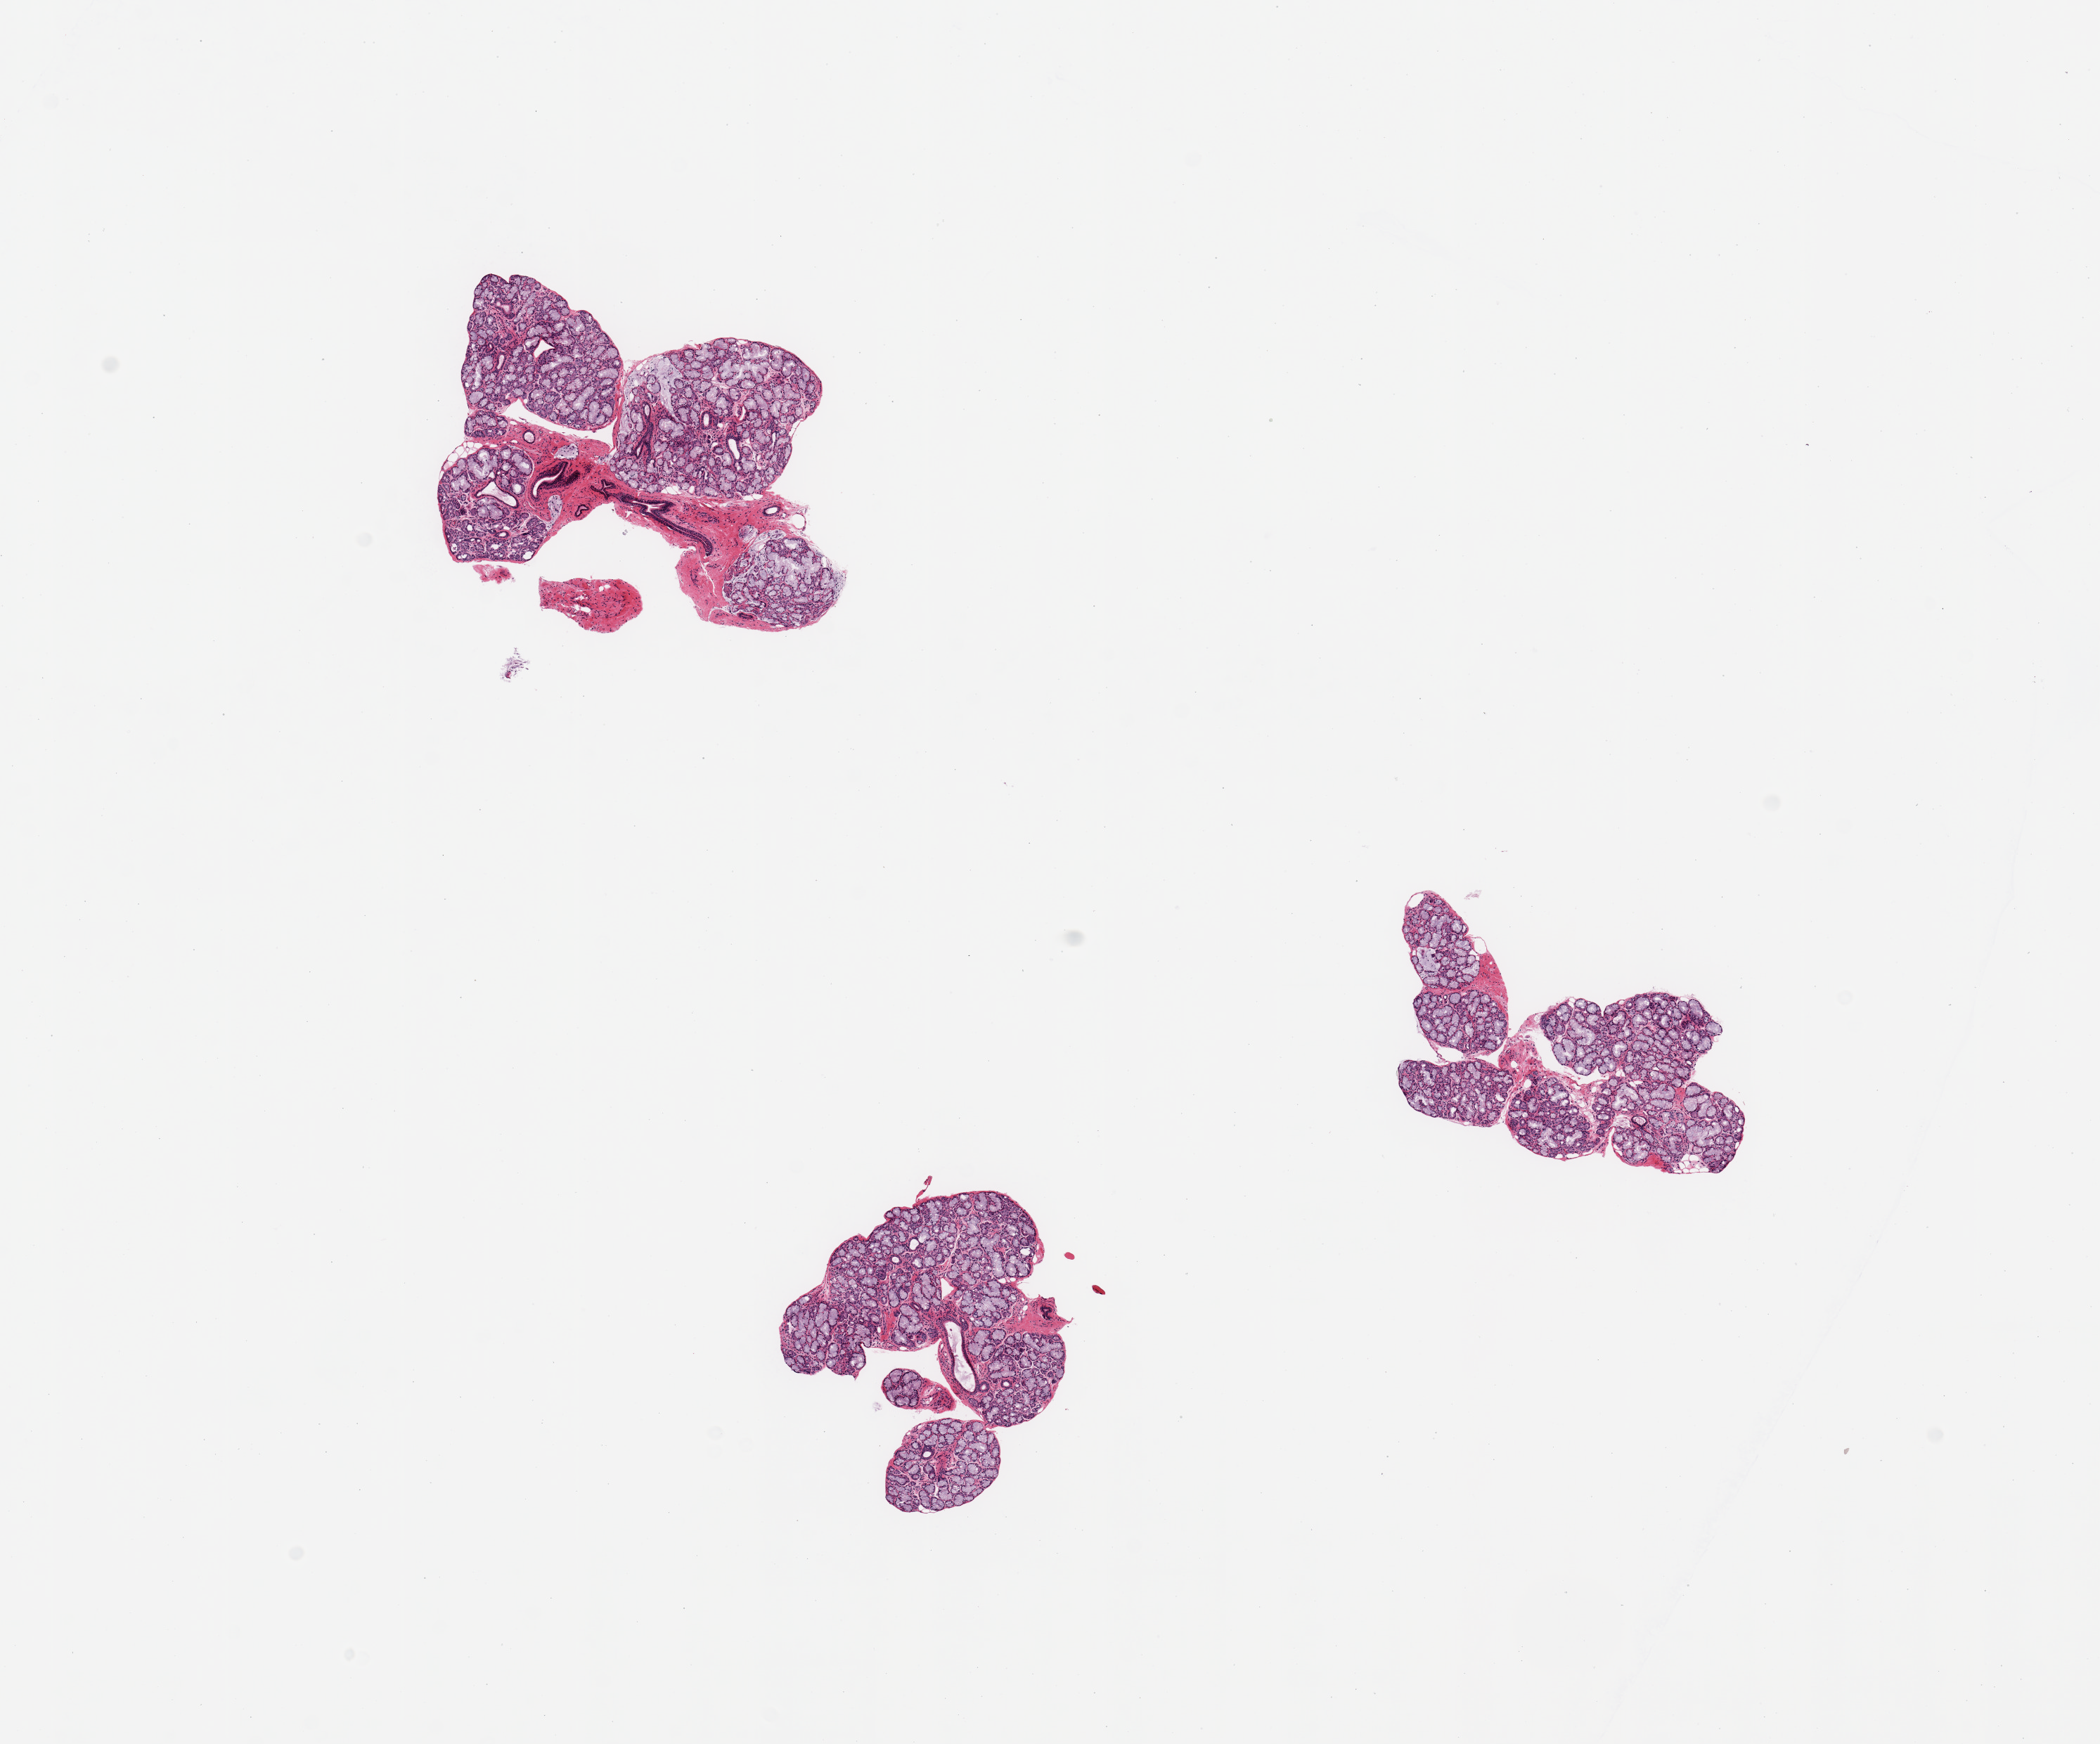
H&E whole-slide image, whole scanned area (about 11.8 x 9.8 mm) shown as a low-resolution overview. PAXgene-fixed paraffin-embedded (PFPE) section. Section of minor salivary gland (target tissue). Donor tissue sample. Donor sex: female.
Pathologist's review note for this sample: 3 pieces; well dissected glands.